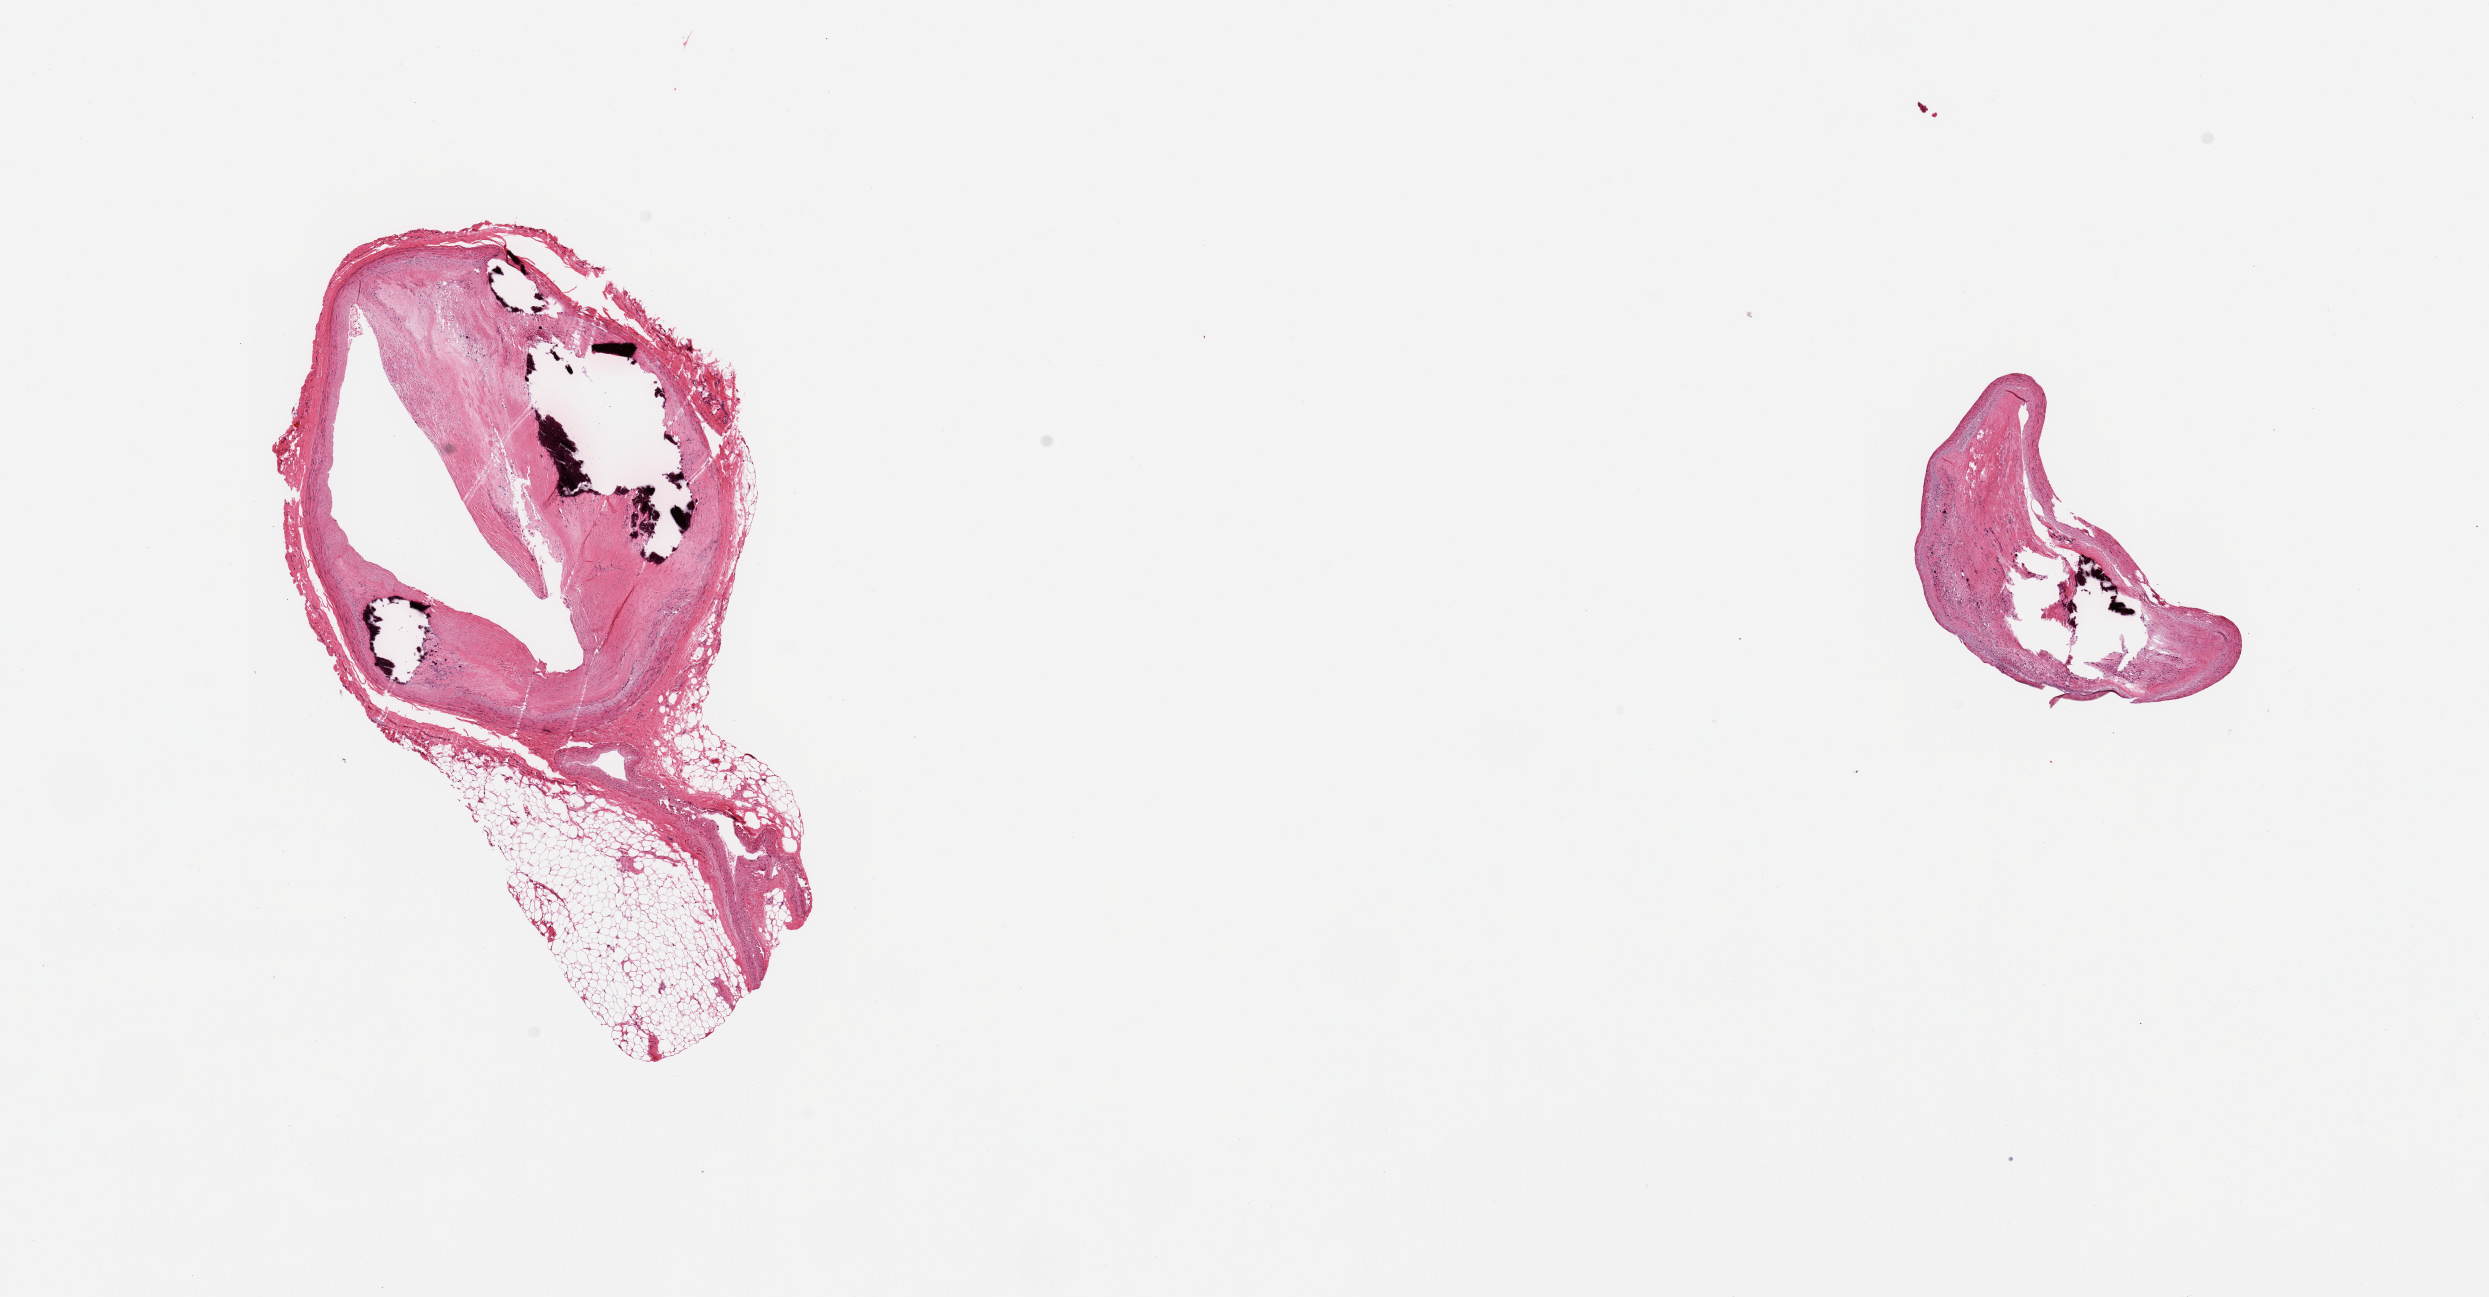
Whole-slide image, H&E stain, whole scanned area (about 19.7 x 10.3 mm, slide scanned at 20x) shown as a low-resolution overview, PAXgene-fixed, paraffin-embedded tissue, sampled site (target tissue): coronary artery, donor tissue sample. Male donor.
• reviewer comment on this tissue sample: 2 pieces; heavily atherosclerotic with prominent calcific deposits; 40% external fat on 1; minimal normal tissue